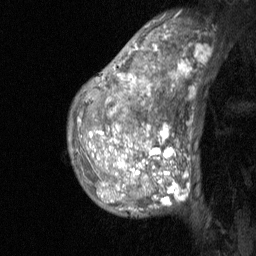
Breast MRI (dynamic contrast-enhanced), one sagittal slice. Position 44 of 64 along the scan axis. Dynamic contrast-enhanced study with each time point stored as its own series, time point 2 of 3 at this slice position (early post-contrast, ordered by acquisition time). 1.5 T. TE 4.8 ms, TR 27 ms. 2 mm slice thickness. 256 × 256 image matrix, field of view 180 × 180 mm. Patient: female, 36 years. From the clinical record (not read from this slice): setting: breast cancer imaged before/during neoadjuvant chemotherapy; receptor status: HR-positive, HER2-negative.
Outlined on this slice (semi-automatic segmentation, software-assisted and operator-edited):
- analysis volume of interest (the breast-tissue region the enhancement analysis was run in; not a lesion): box from (x=68, y=14) to (x=195, y=218) px
- tumour enhancement mask (voxels above the 90 % enhancement threshold inside the analysis volume of interest): (x=90, y=46)–(x=179, y=203)